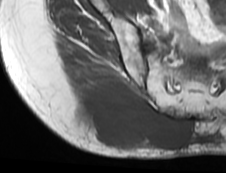
MRI of an extremity soft-tissue mass, one axial slice; slice 47 of 73 in the series (ordered by position); MR volume resampled by the dataset authors to the PET/CT grid (not the native acquisition matrix); 226 × 173 image matrix. Female patient. From the clinical record (not read from this slice): histological type: spindle cell suggestive of myxofibrosarcoma; grade: intermediate; site of the primary tumour: right buttock.
Outlined on this slice (expert contour drawn on MRI and transferred to this co-registered scan by the dataset authors):
- gross tumour volume (mass): bounding box (x1, y1, x2, y2) in pixels: (70, 81, 190, 150)